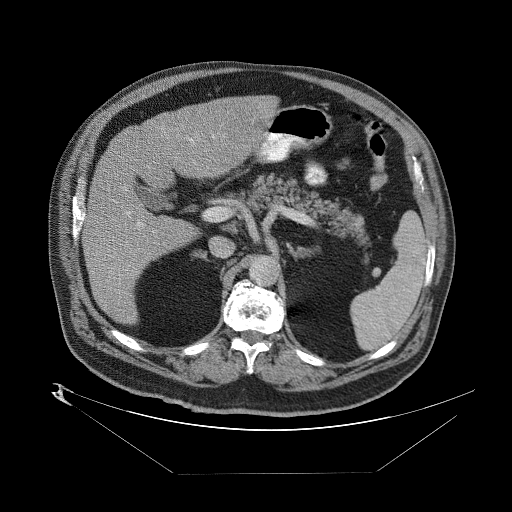
Contrast-enhanced abdominal CT (liver protocol), one axial slice. Position 40 of 89 along the scan axis. Reconstruction kernel STANDARD. One of 2 acquisitions stored at this slice position. Soft-tissue window (W 400 / L 40 HU). 512 × 512 image matrix, field of view 480 × 480 mm. Case-level facts recorded for this patient, not image findings: diagnosis: hepatocellular carcinoma (patient treated with transarterial chemoembolisation; whether this scan precedes or follows treatment is not stated here); TNM stage (as recorded): Stage-II.
Structures marked on this image (semi-automatic segmentation, software-assisted and operator-edited):
- abdominal aorta: box from (x=250, y=257) to (x=277, y=284) px
- liver parenchyma outside the tumour (the mass and vessels are separate outlines, so this box may not span the whole liver): (x=82, y=92)–(x=272, y=328)
- liver vessels: (x=114, y=130)–(x=224, y=283)